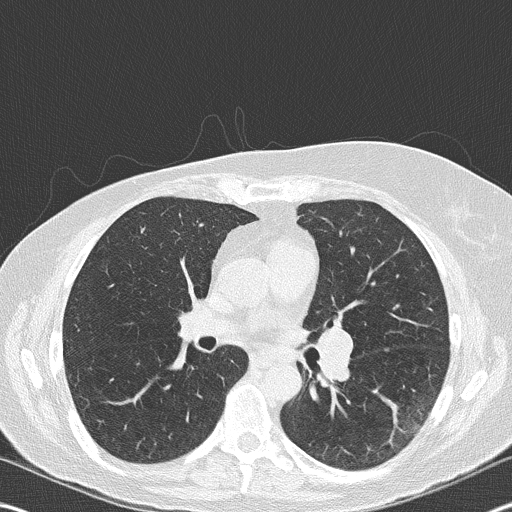
Low-dose screening chest CT, one axial slice. Slice 100 of 177 in the series (ordered by position). 120 kVp. Lung window (W 1500 / L -600 HU). 2 mm slice thickness. 512 × 512 image matrix.
Structures marked on this image (outlined manually by an expert reader):
- lesion 2 (nodule, hilum of left lung): bounding box (x1, y1, x2, y2) in pixels: (319, 326, 354, 380)